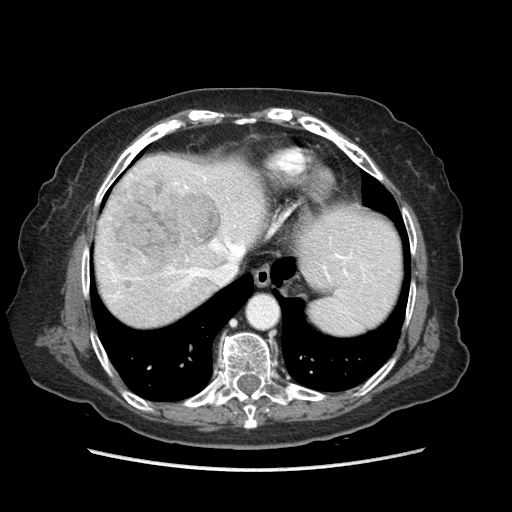
Contrast-enhanced abdominal CT (liver protocol), one axial slice; slice 70 of 89 in the series (ordered by position); reconstruction kernel STANDARD; soft-tissue window (W 400 / L 40 HU); 512 × 512 image matrix, field of view 360 × 360 mm. From the clinical record (not read from this slice): diagnosis: hepatocellular carcinoma (patient treated with transarterial chemoembolisation; whether this scan precedes or follows treatment is not stated here); TNM stage (as recorded): Stage-IIIA; Child-Pugh class: A; tumour differentiation: well differentiated; tumour nodularity: multinodular.
Structures marked on this image (semi-automatically segmented with operator editing):
- abdominal aorta: bounding box <249,297,277,328> (left, top, right, bottom; pixels)
- liver parenchyma outside the tumour (the mass and vessels are separate outlines, so this box may not span the whole liver): <94,154,400,326>
- mass: <97,177,221,290>
- liver vessels: <108,172,352,298>